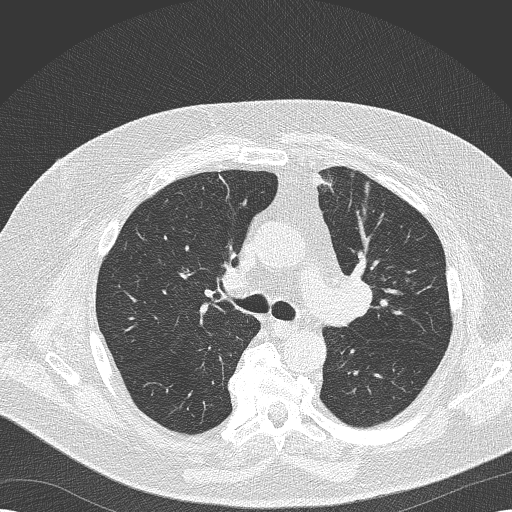
Axial slice from a low-dose chest CT screening exam. Second screening round (one year after baseline). Lung window (W 1500 / L -600 HU). Lung (sharp) reconstruction kernel (B50f). Slice 65 of 173 in the series. Male participant, aged 68 years at enrolment. Former smoker at enrolment.
• Expert reader's lesion annotation, bounding box (x1, y1, x2, y2) in pixels: (322, 267, 377, 331).
• The exam's reader record, not a measurement of the box and not confirmed to be the same lesion: non-calcified nodule or mass ≥4 mm, left lower lobe, 8 × 6 mm, soft tissue attenuation, pre-existing on the prior screen: yes; interval growth: no.
• Official screen result: positive, no significant change: stable abnormalities potentially related to lung cancer, unchanged since the prior screening exam.
• Lung cancer was diagnosed 256 days after this screen: squamous cell carcinoma, NOS, left upper lobe, poorly differentiated (G3), stage IIB (AJCC 6th edition), 35 mm at pathology.